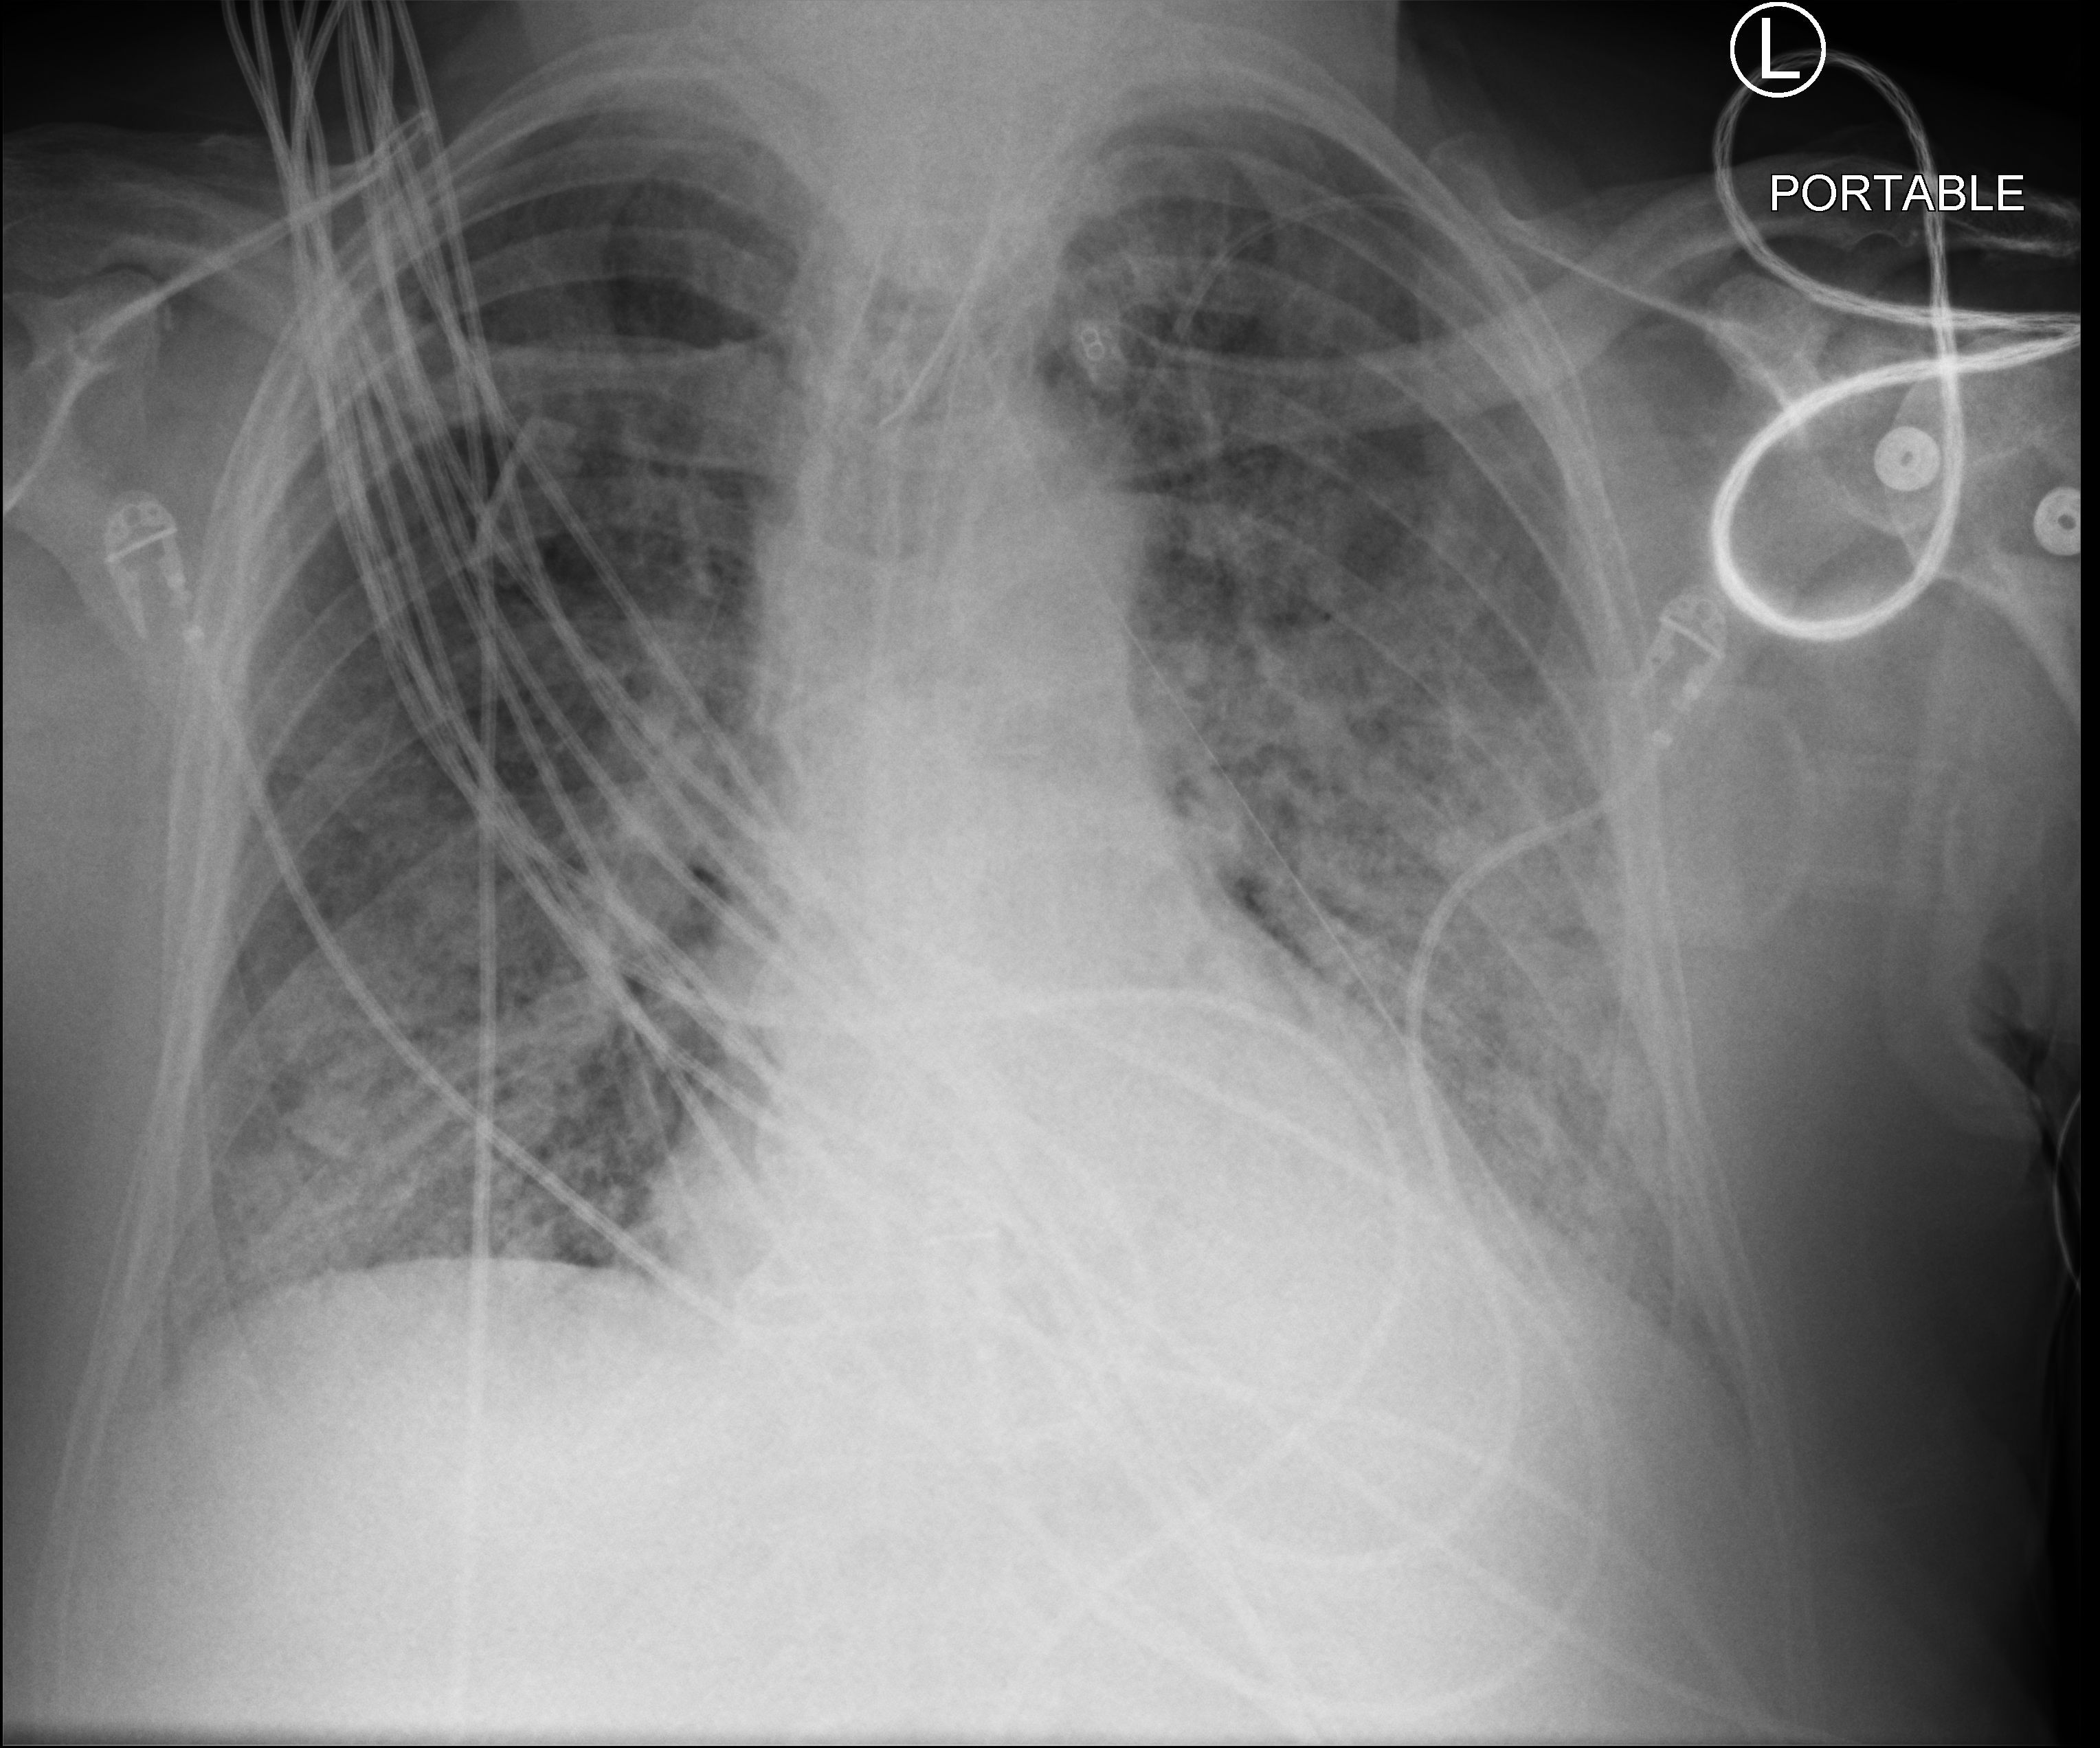
Bedside chest radiograph (computed radiography); anteroposterior (AP) projection. Patient hospitalised with COVID-19; male, aged 75–90 years.
Hospital-stay facts (about this admission, not read from this image; timing relative to this image not recorded): length of hospital stay: 14 days; admitted to intensive care during this hospital stay: yes; mechanically ventilated during this hospital stay: yes.